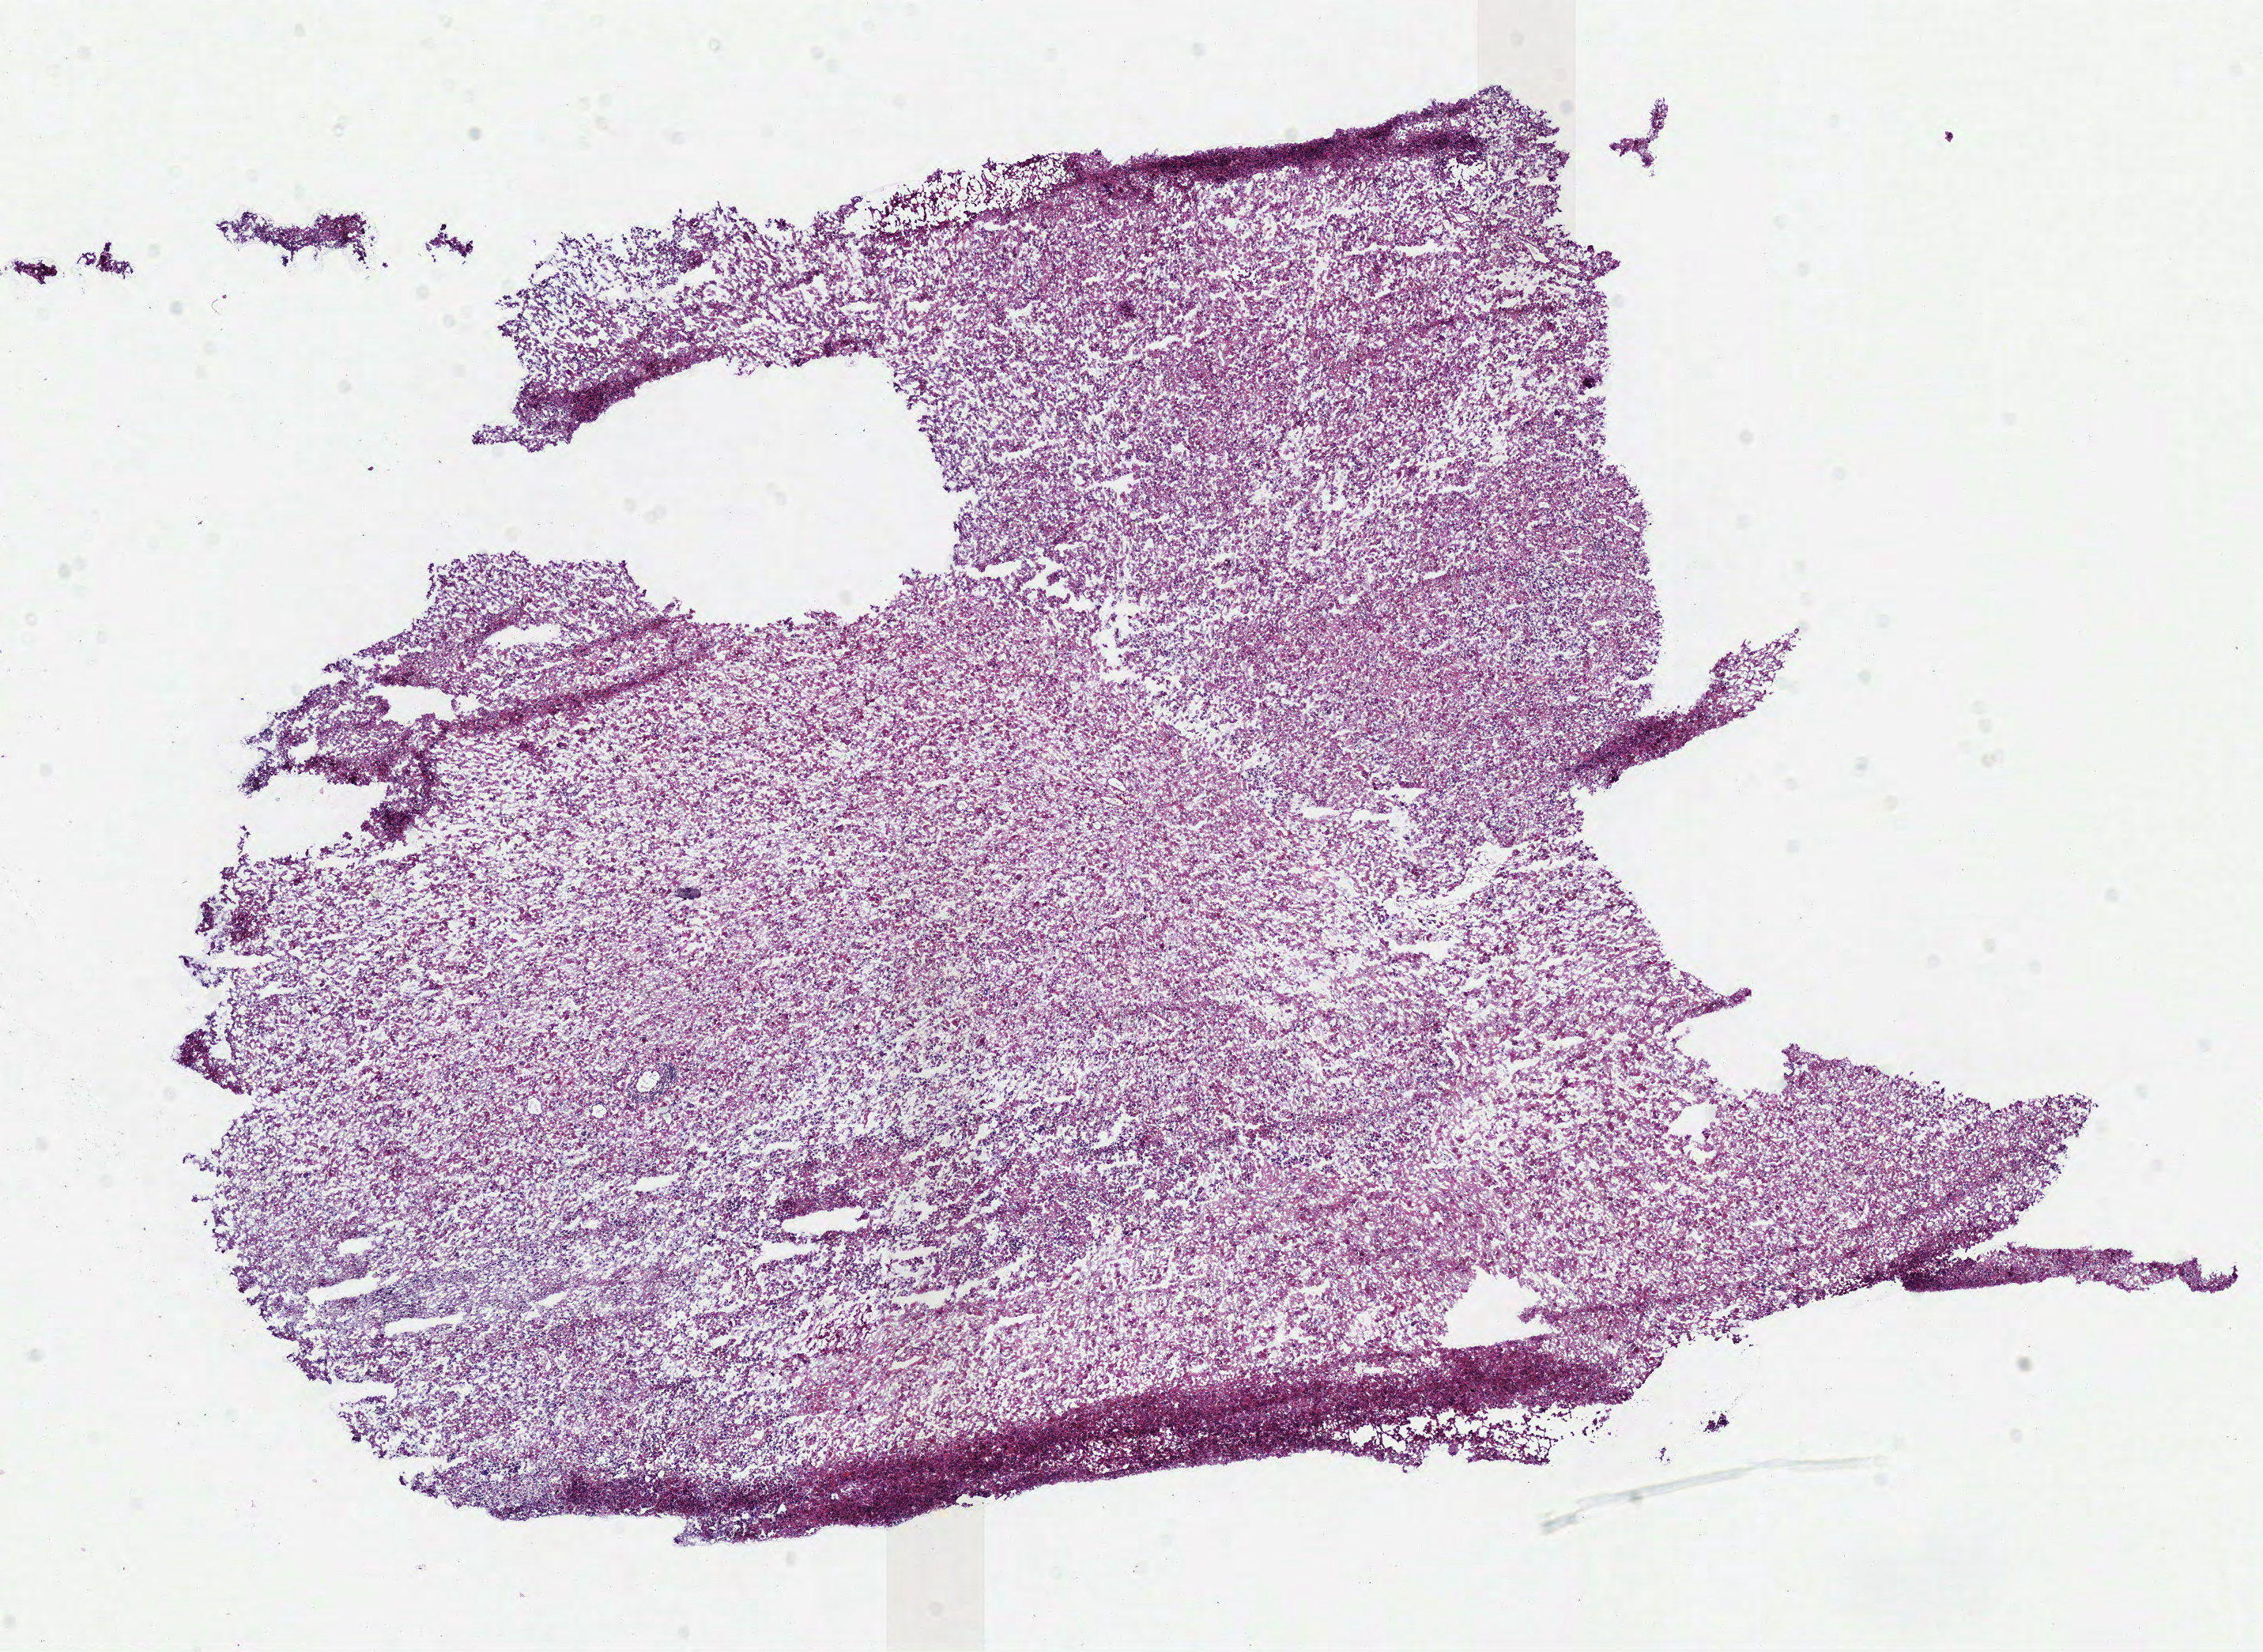
Digitized Hematoxylin and eosin (H&E) stained tissue section (whole slide) — shown as a low-resolution overview of the whole scanned area (about 11.3 x 8.2 mm, acquisition: 40x scan), frozen section from the bottom of the tissue portion, sample: primary tumour, brain. Male, age 33 years at initial diagnosis.
Diagnosis: Astrocytoma, NOS (cerebrum).